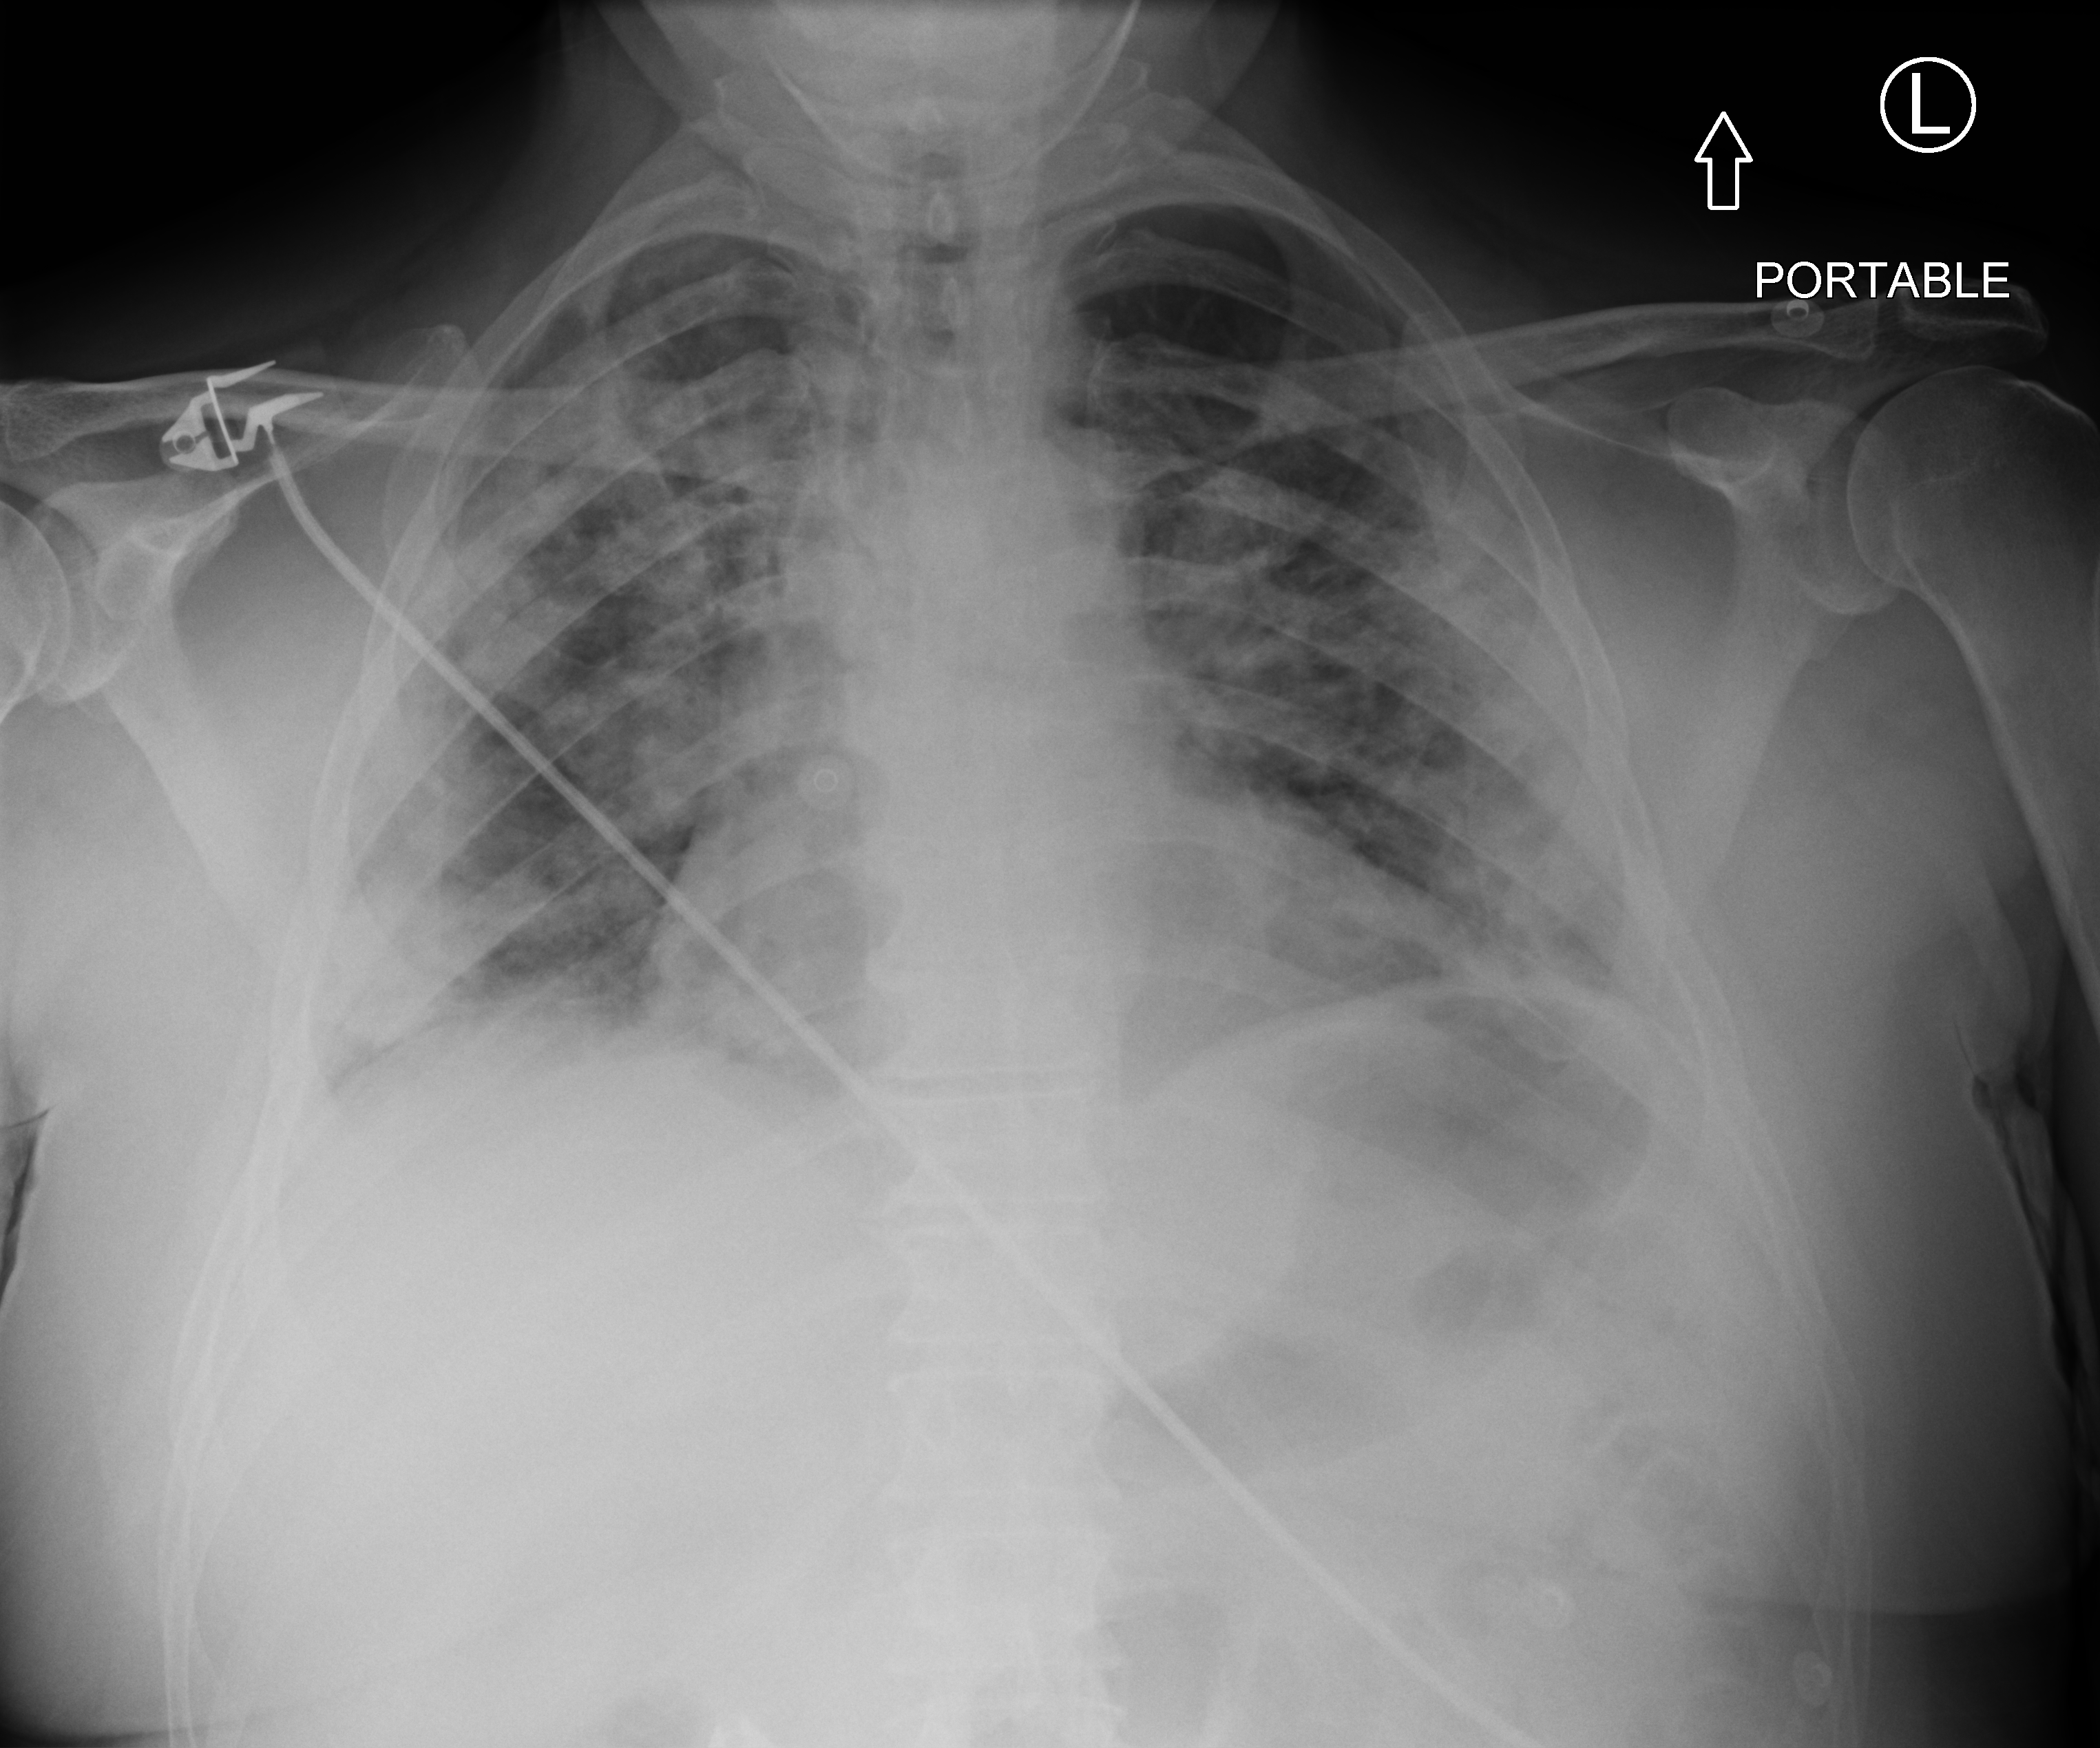
Portable chest radiograph, anteroposterior (AP) projection. Patient hospitalised with COVID-19; male, aged 18–59 years.
Admission-level facts for this patient (not findings on this image; timing relative to this image not recorded): smoking status (admission record): never; mechanically ventilated during this hospital stay: no.